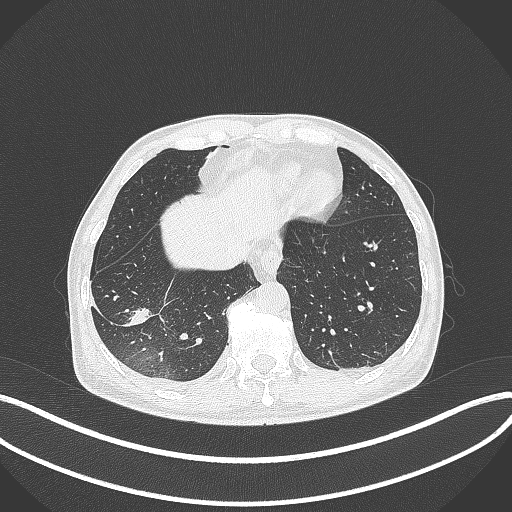
Chest CT, one axial slice. Position 86 of 388 along the scan axis. Lung window (W 1500 / L -600 HU). 1 mm slice thickness. 512 × 512 image matrix, field of view 400 × 400 mm. Male patient, age 64 years. Case-level facts recorded for this patient, not image findings: clinical TNM (as recorded): T3 N0 M0.
Outlined on this slice (bounding box drawn by a radiologist):
- lung tumour (recorded histology: adenocarcinoma): box from (x=121, y=302) to (x=155, y=334) px